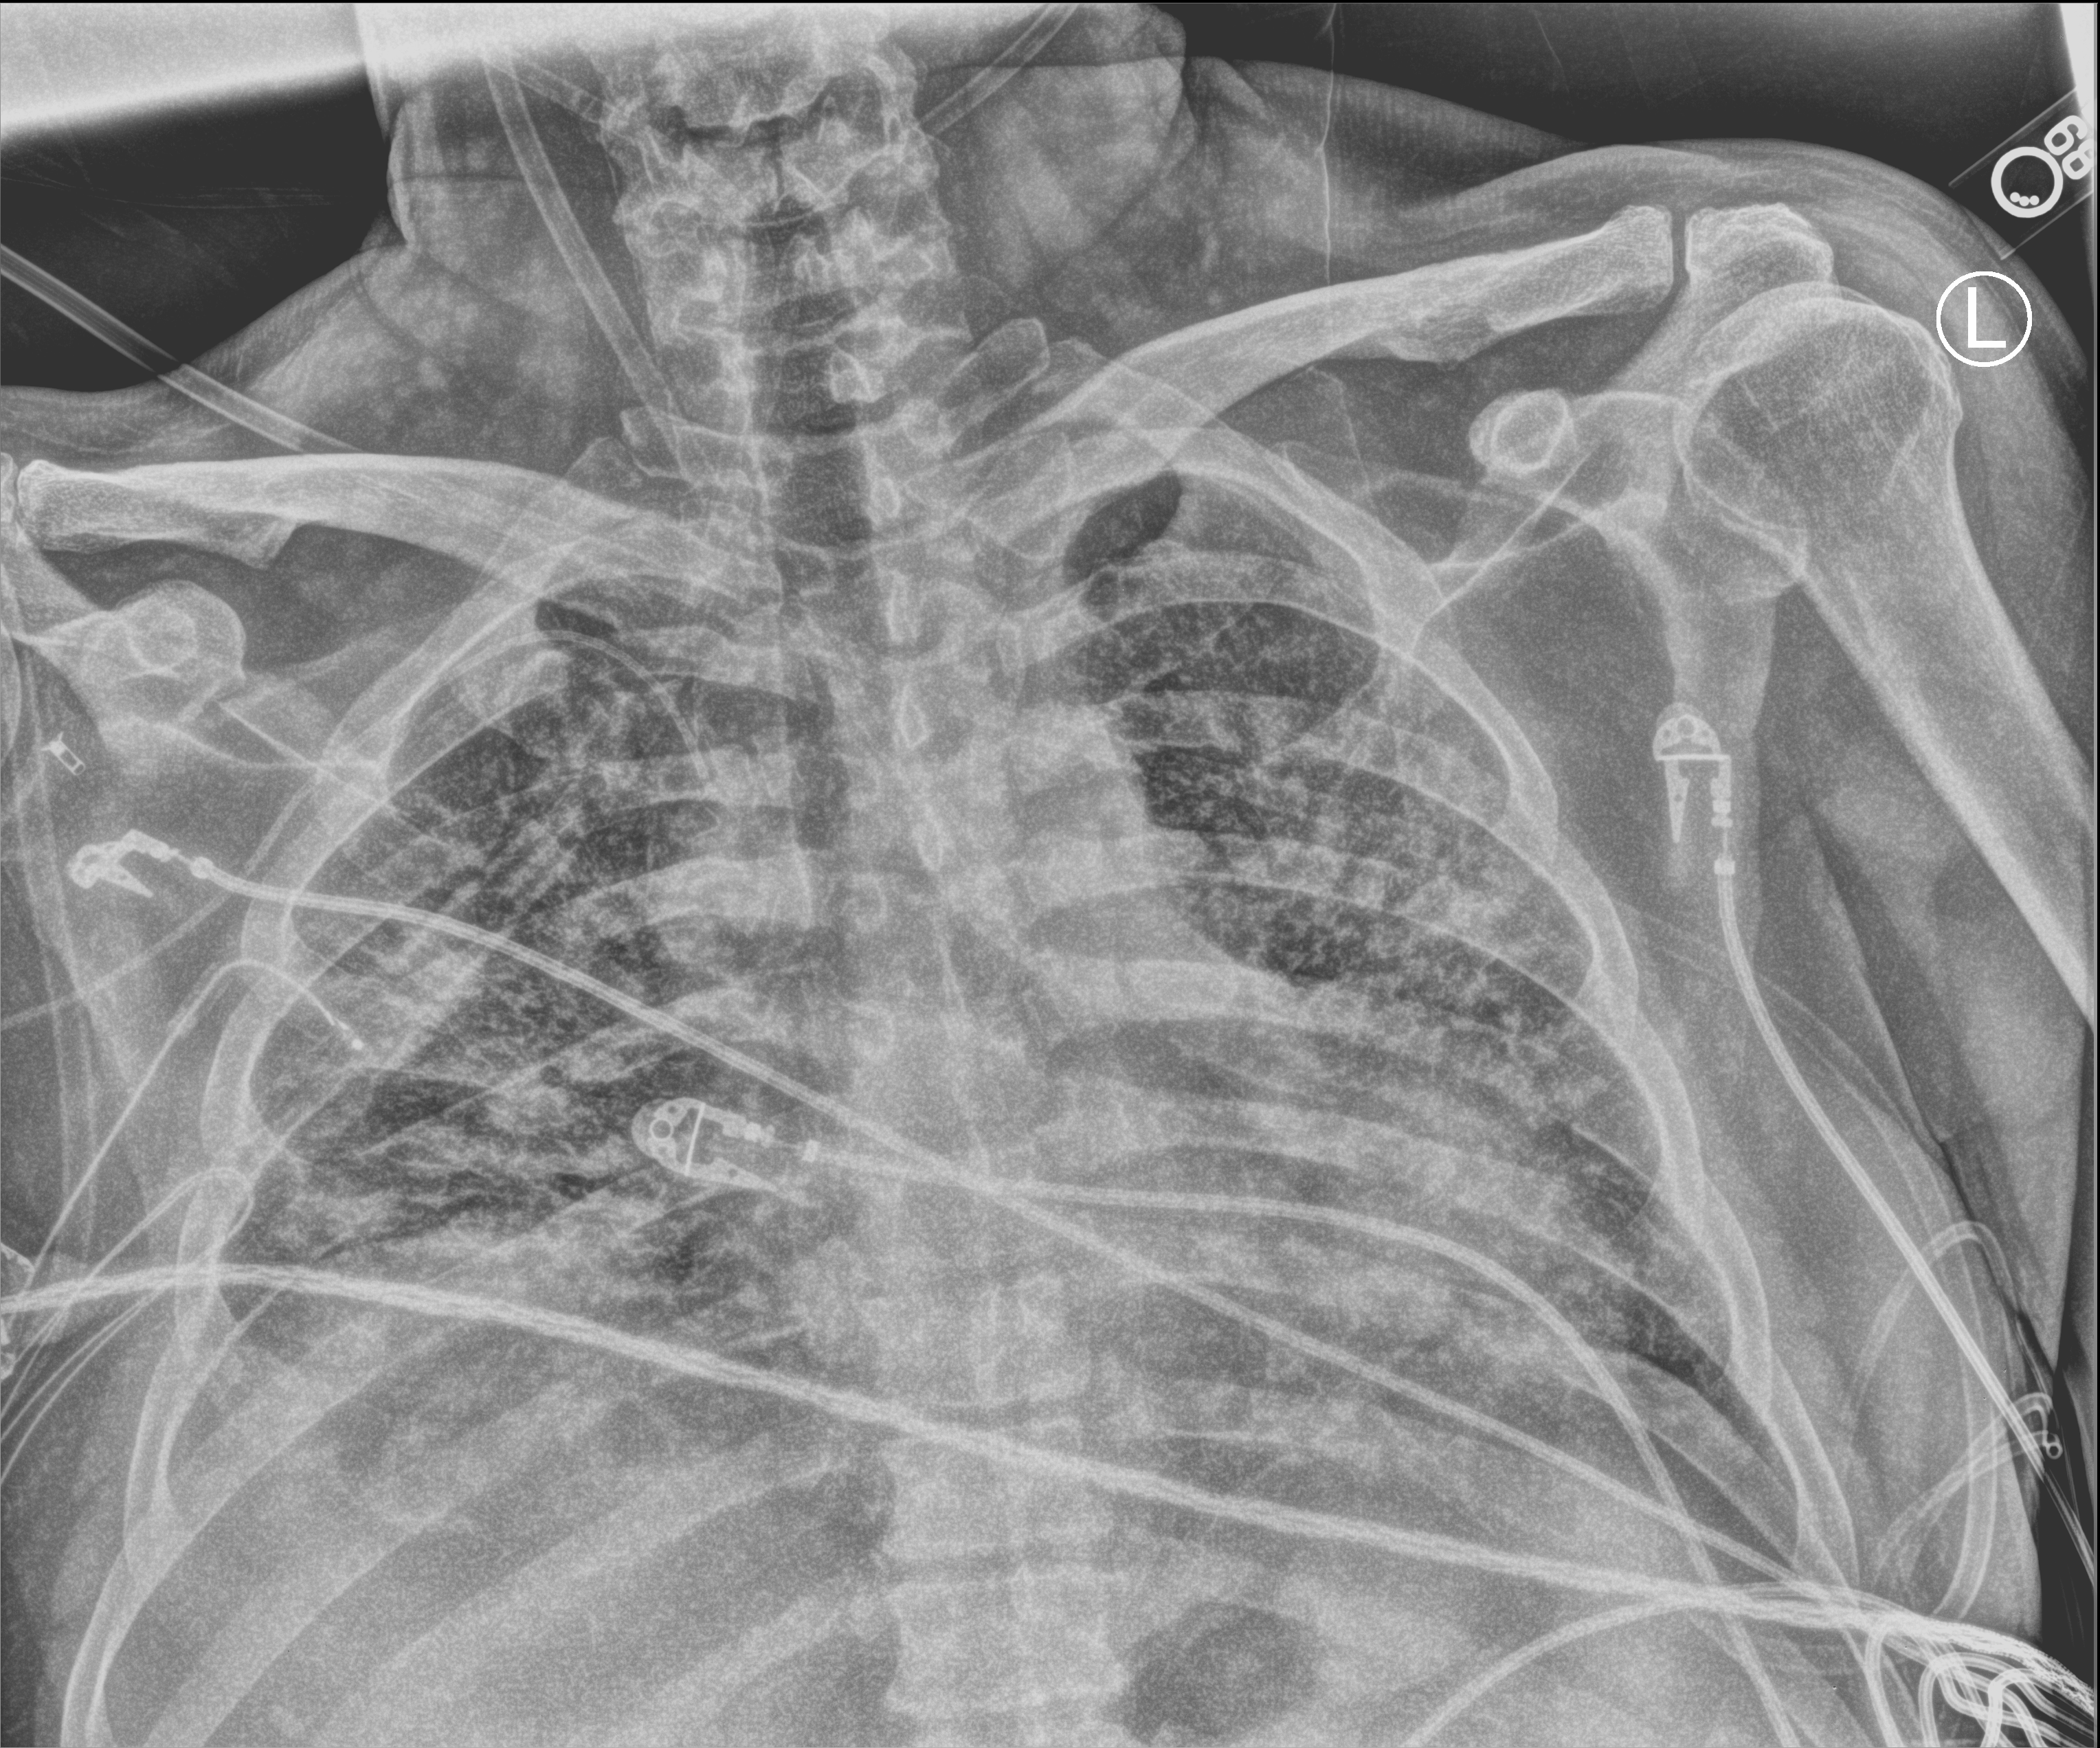
Portable chest radiograph. Male patient hospitalised with COVID-19, age 18–59 years.
From the hospital-stay record, not from the radiograph (when in the stay this image was taken is not recorded): admitted to intensive care during this hospital stay: yes.